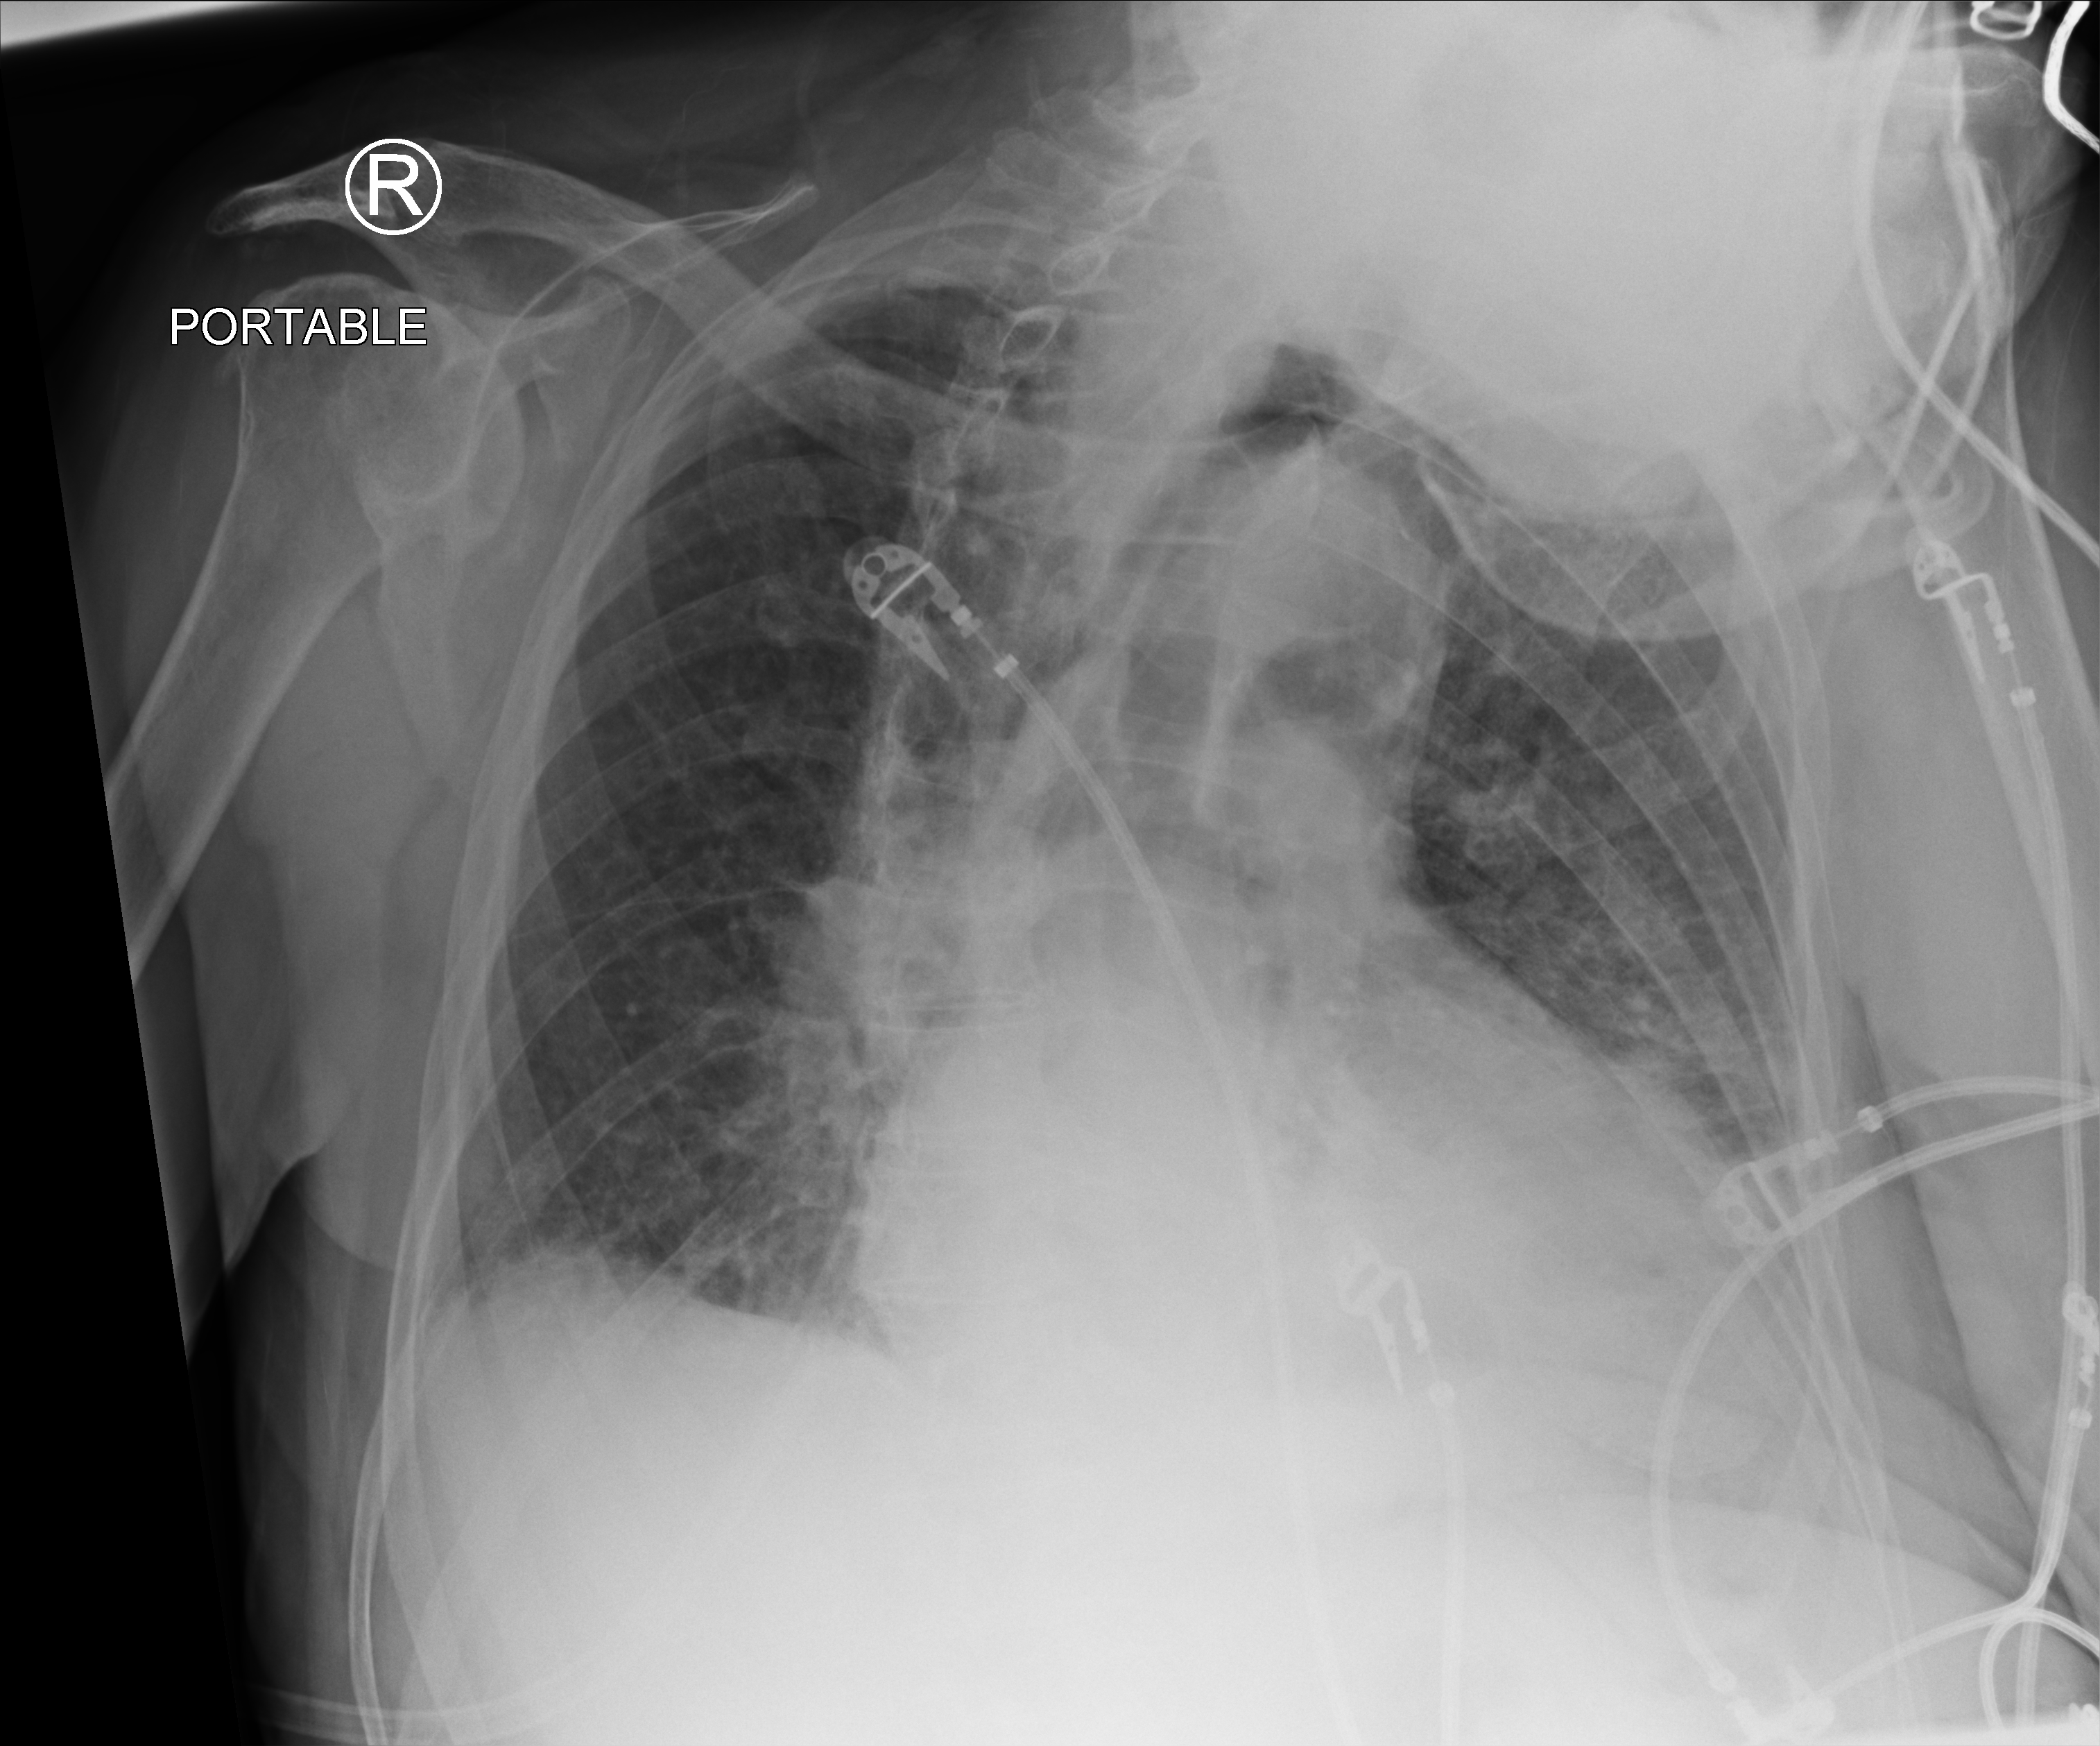
Chest X-ray (portable); anteroposterior (AP) projection. Male patient hospitalised with COVID-19, age 75–90 years.
From the hospital-stay record, not from the radiograph (when in the stay this image was taken is not recorded): smoking status (admission record): never.